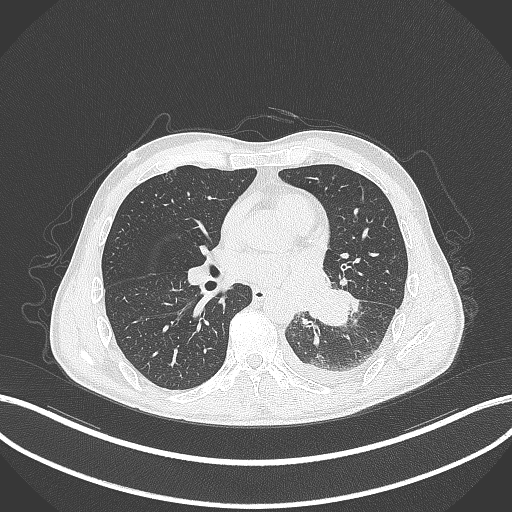
Chest CT, one axial slice; slice 151 of 295 in the series (ordered by position); reconstruction kernel B70f; 120 kVp; lung window (W 1500 / L -600 HU); 1 mm slice thickness; 512 × 512 image matrix, field of view 400 × 400 mm. Male patient, age 47 years. Case-level facts recorded for this patient, not image findings: clinical TNM (as recorded): T3 N1 M1c; histopathological grade: G3.
Structures marked on this image (rectangle marked by the reading radiologist):
- lung tumour (recorded histology: small cell carcinoma): bounding box <303,287,347,327> (left, top, right, bottom; pixels)